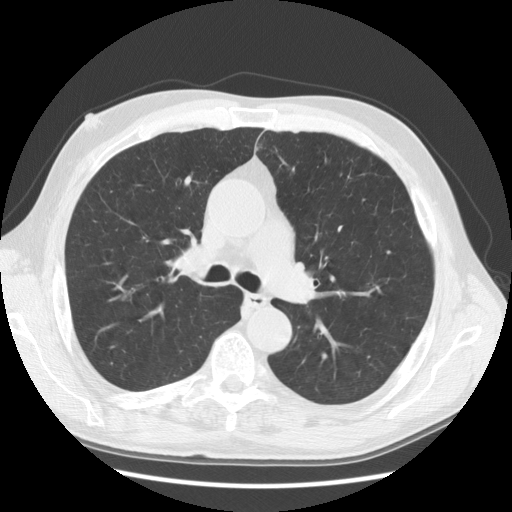
Chest CT (low-dose screening protocol), one axial image, first (baseline) screen, lung window (W 1500 / L -600 HU), 2.5 mm slice thickness, standard (soft-tissue) reconstruction kernel (STANDARD), 140 kVp, slice 56 of 145 in the series. Male participant, aged 60 years at enrolment. Current smoker at enrolment.
Expert-annotated lung lesion, bounding box (x1, y1, x2, y2) in pixels: (156, 229, 214, 284). Screening reader's record for this exam: no non-calcified nodule ≥4 mm recorded. Participant outcome: lung cancer diagnosed 193 days after this screen — squamous cell carcinoma, NOS, right upper lobe, moderately differentiated (G2), stage IIIB (AJCC 6th edition), 52 mm at pathology.